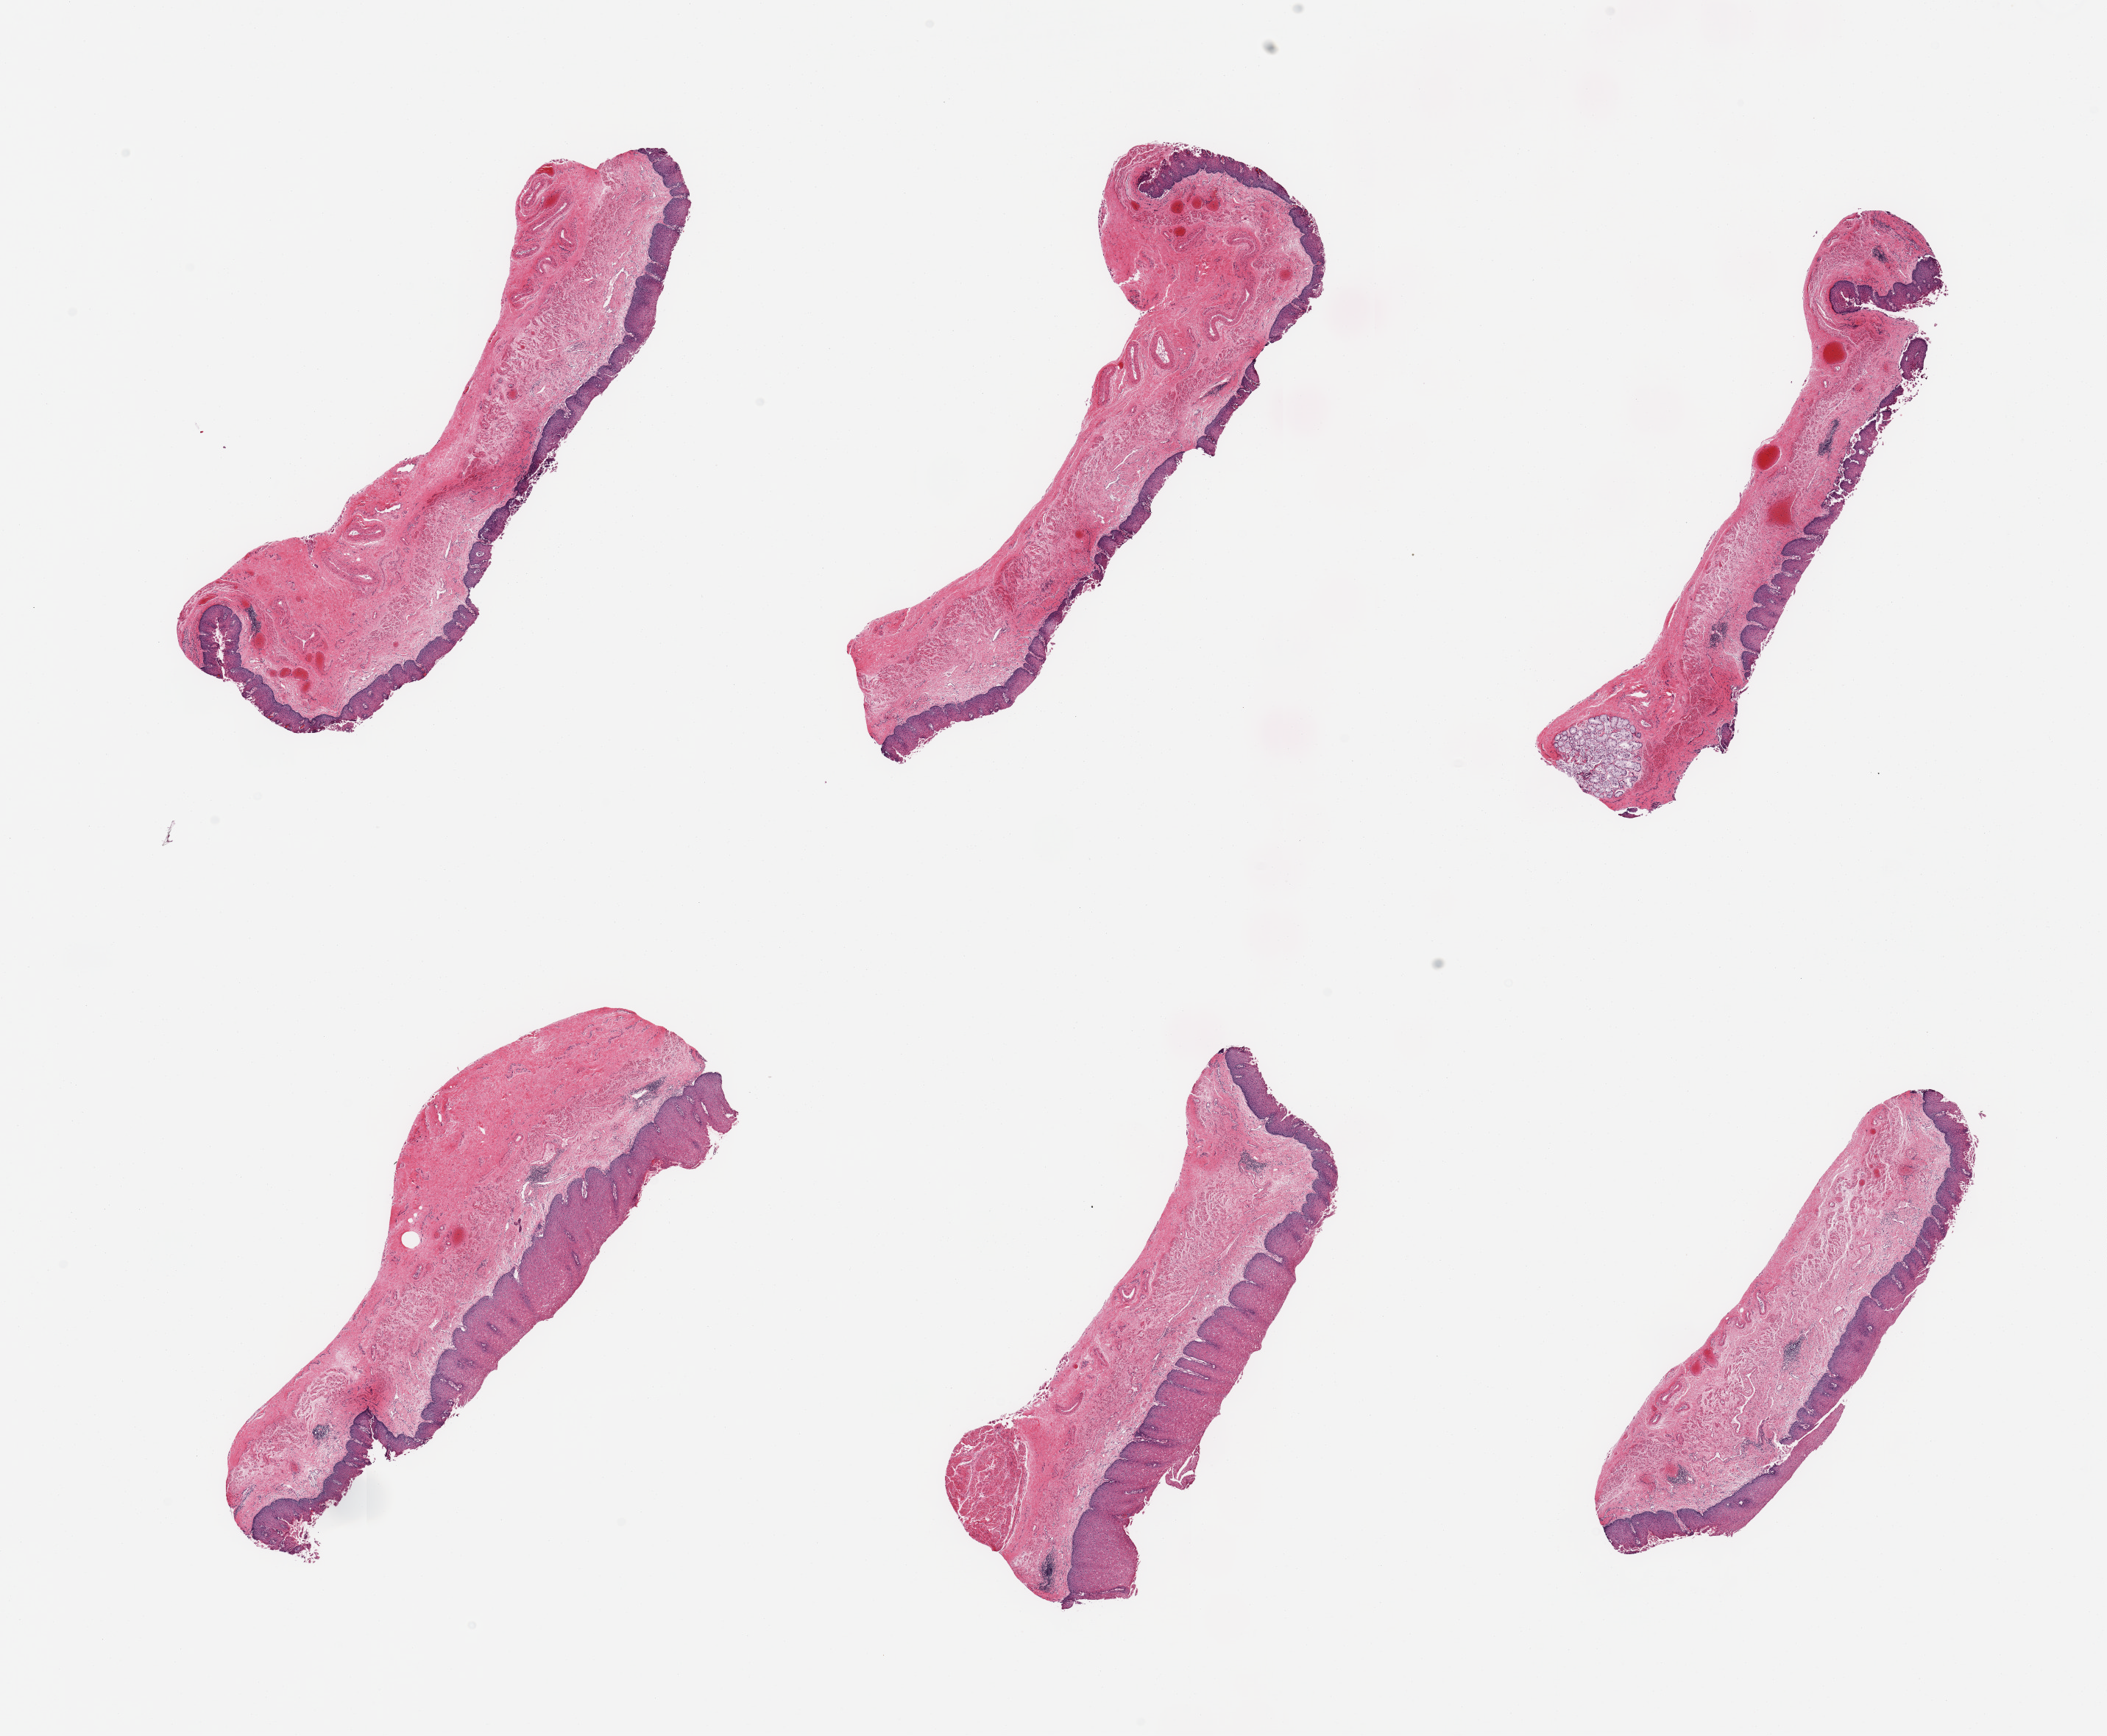
Whole-slide image, haematoxylin and eosin stain — whole scanned area (about 22.6 x 18.7 mm, slide scanned at 20x) shown as a low-resolution overview; PAXgene-fixed, paraffin-embedded tissue; target tissue: esophageal mucous membrane; tissue donor sample. Male donor.
Reviewer comment on this tissue sample: 6 pieces, squamous mucosa up to ~0.6mm, 30-40% thickness; Submucosal mucus gland; Few foci with more moderate autolysis, early sloughing.